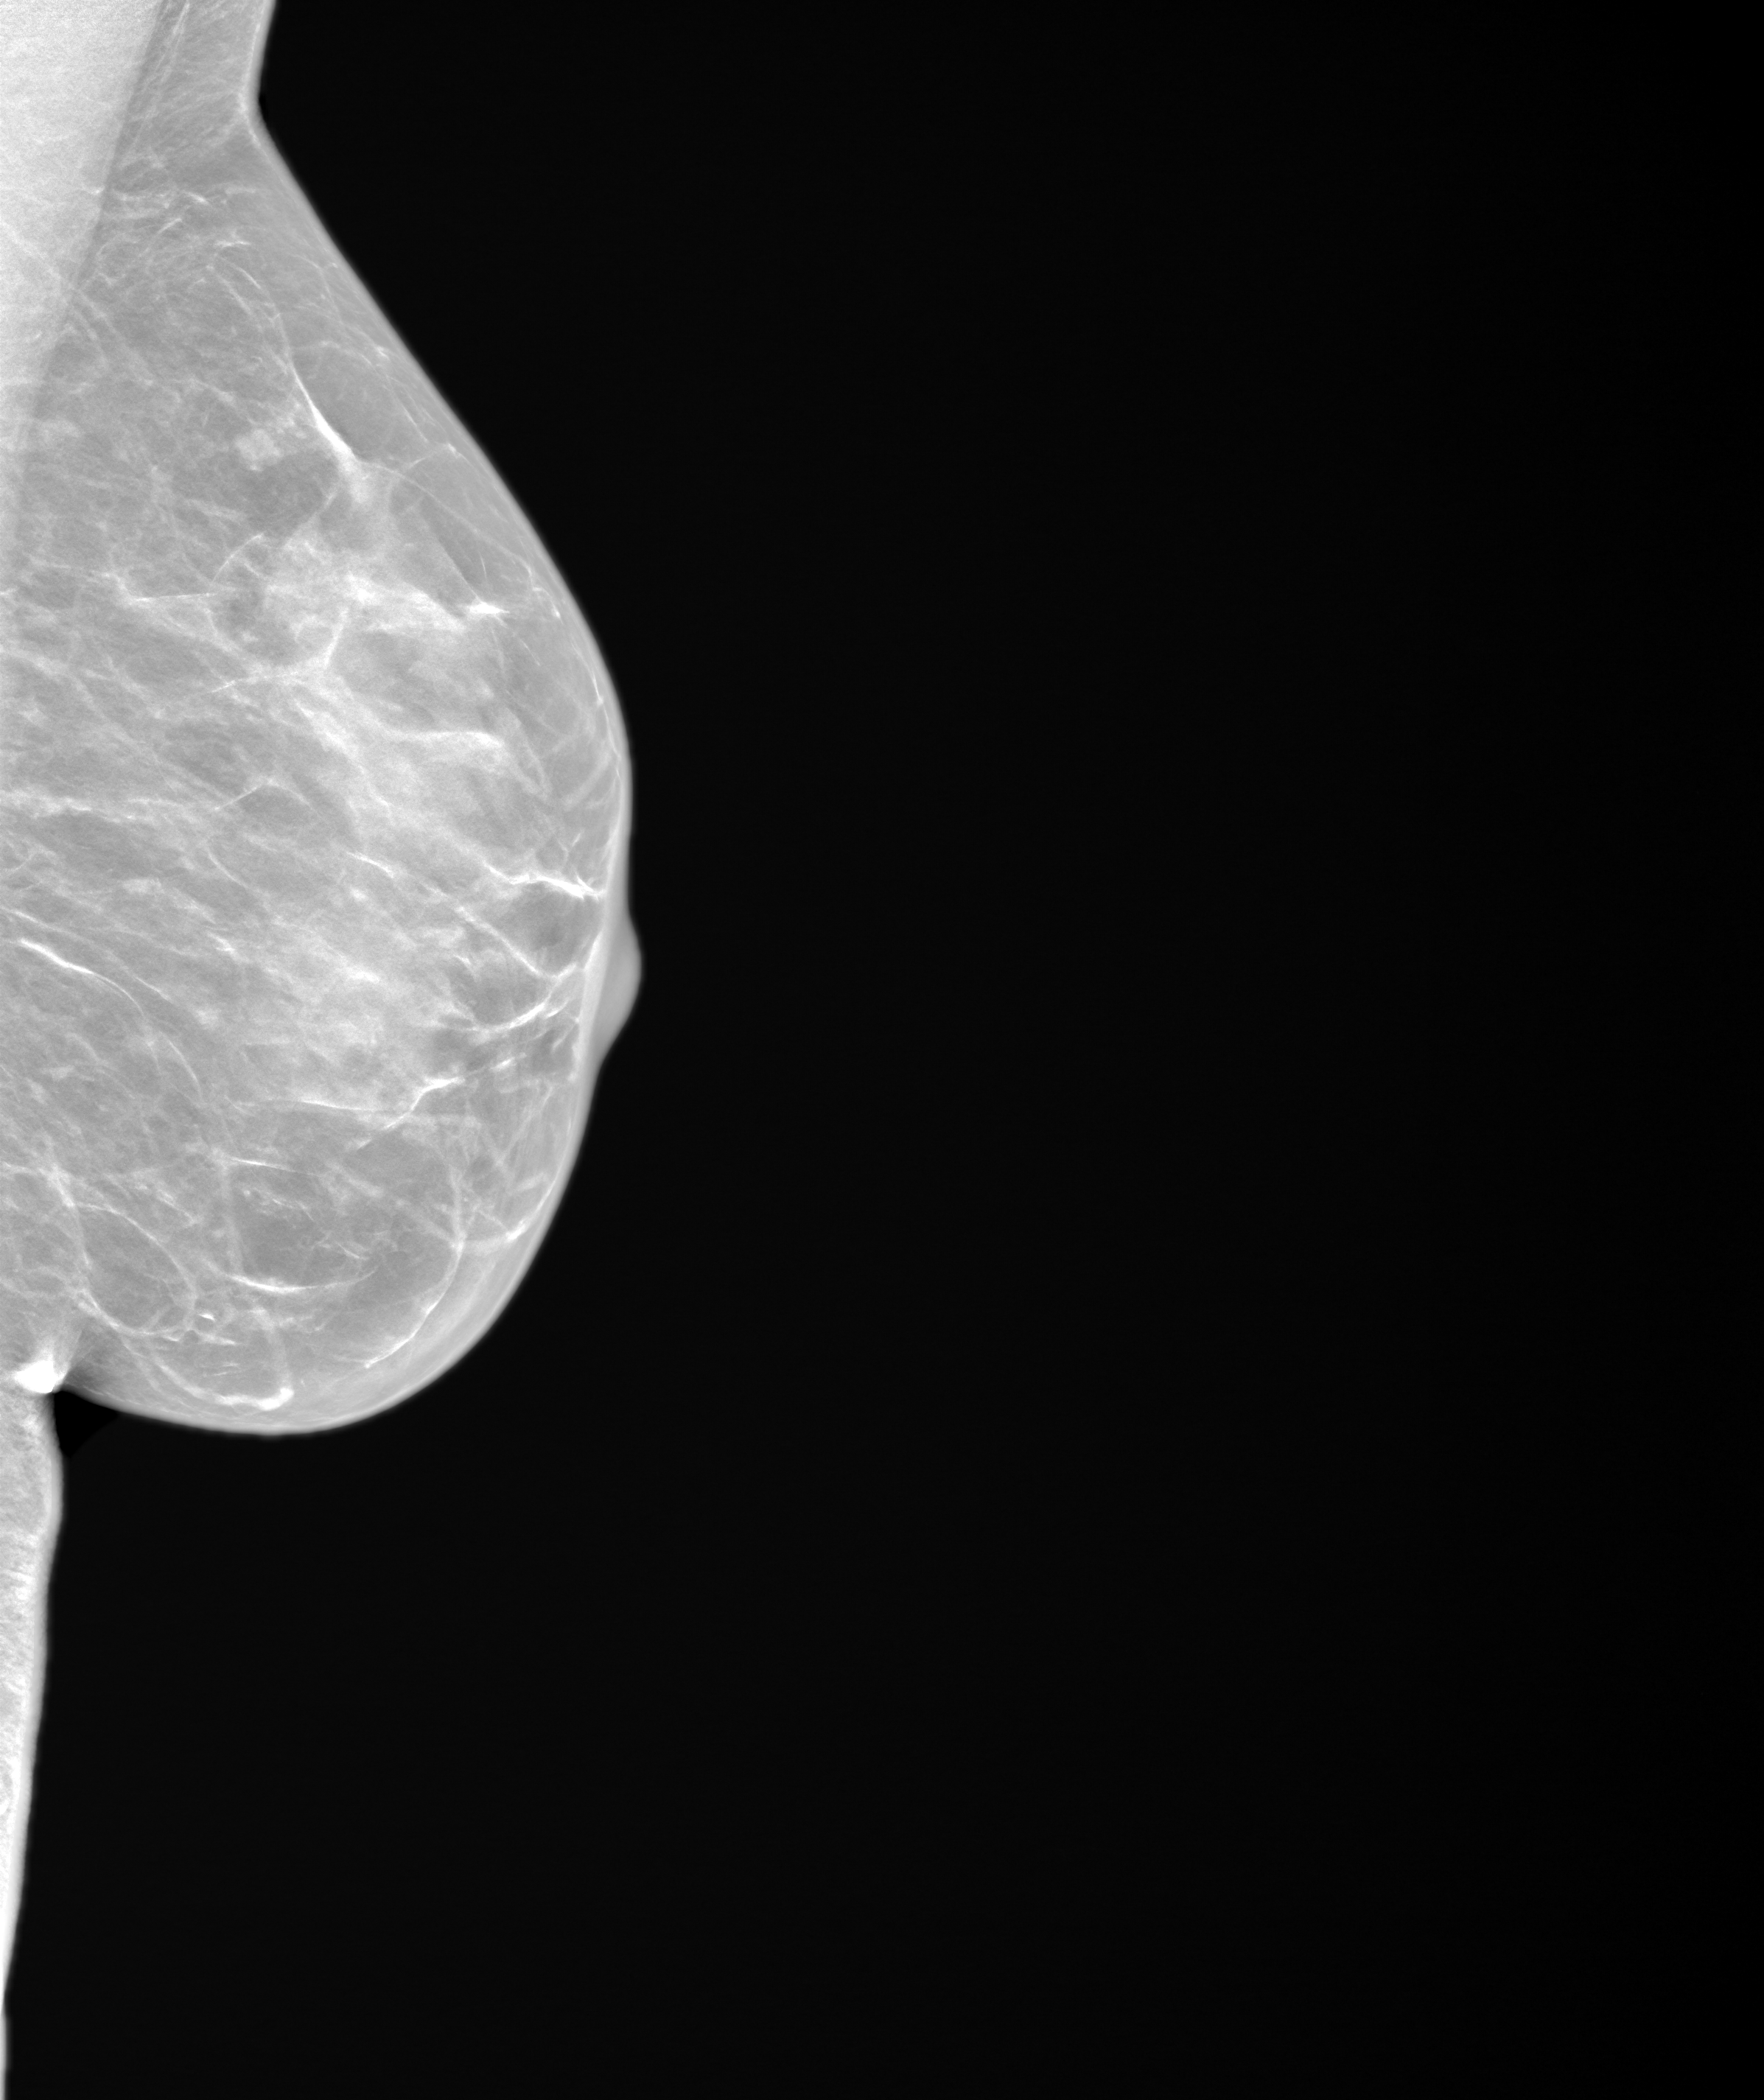
Screening examination, system: SenoIris_1SP1.1(421). Female patient, age 47 years.
Image type: synthesized 2-D view from tomosynthesis. Breast: left. Projection: medio-lateral oblique projection.